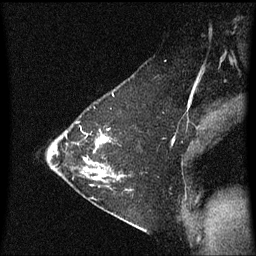
Breast MRI (dynamic contrast-enhanced), one sagittal slice. Position 43 of 60 along the scan axis. Dynamic contrast-enhanced series, image 2 of 3 at this slice position (ordered by acquisition). 1.5 T. TE 4.2 ms, TR 8.4 ms. 2 mm slice thickness. 256 × 256 image matrix, field of view 200 × 200 mm. Female patient, age 36 years. From the clinical record (not read from this slice): setting: breast cancer imaged before/during neoadjuvant chemotherapy; receptor status: HR-positive, HER2-negative.
Outlined on this slice (semi-automatically segmented with operator editing):
- analysis volume of interest (the breast-tissue region the enhancement analysis was run in; not a lesion): bounding box (x1, y1, x2, y2) in pixels: (72, 116, 123, 187)
- tumour enhancement mask (voxels above the 70 % enhancement threshold inside the analysis volume of interest): (84, 136, 123, 181)